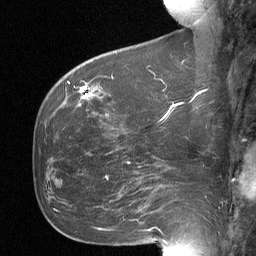
Breast MRI (dynamic contrast-enhanced), one sagittal slice; dynamic contrast-enhanced study with each time point stored as its own series, time point 2 of 3 at this slice position (early post-contrast, ordered by acquisition time); 1.5 T; TE 4.8 ms, TR 27 ms; 256 × 256 image matrix, field of view 200 × 200 mm. Female patient, age 60 years. Case-level facts recorded for this patient, not image findings: setting: breast cancer imaged before/during neoadjuvant chemotherapy; receptor status: HR-positive, HER2-negative.
Outlined on this slice (semi-automatic segmentation, software-assisted and operator-edited):
- analysis volume of interest (the breast-tissue region the enhancement analysis was run in; not a lesion): bounding box (x1, y1, x2, y2) in pixels: (67, 68, 109, 112)
- tumour enhancement mask (voxels above the 90 % enhancement threshold inside the analysis volume of interest): (80, 87, 88, 97)